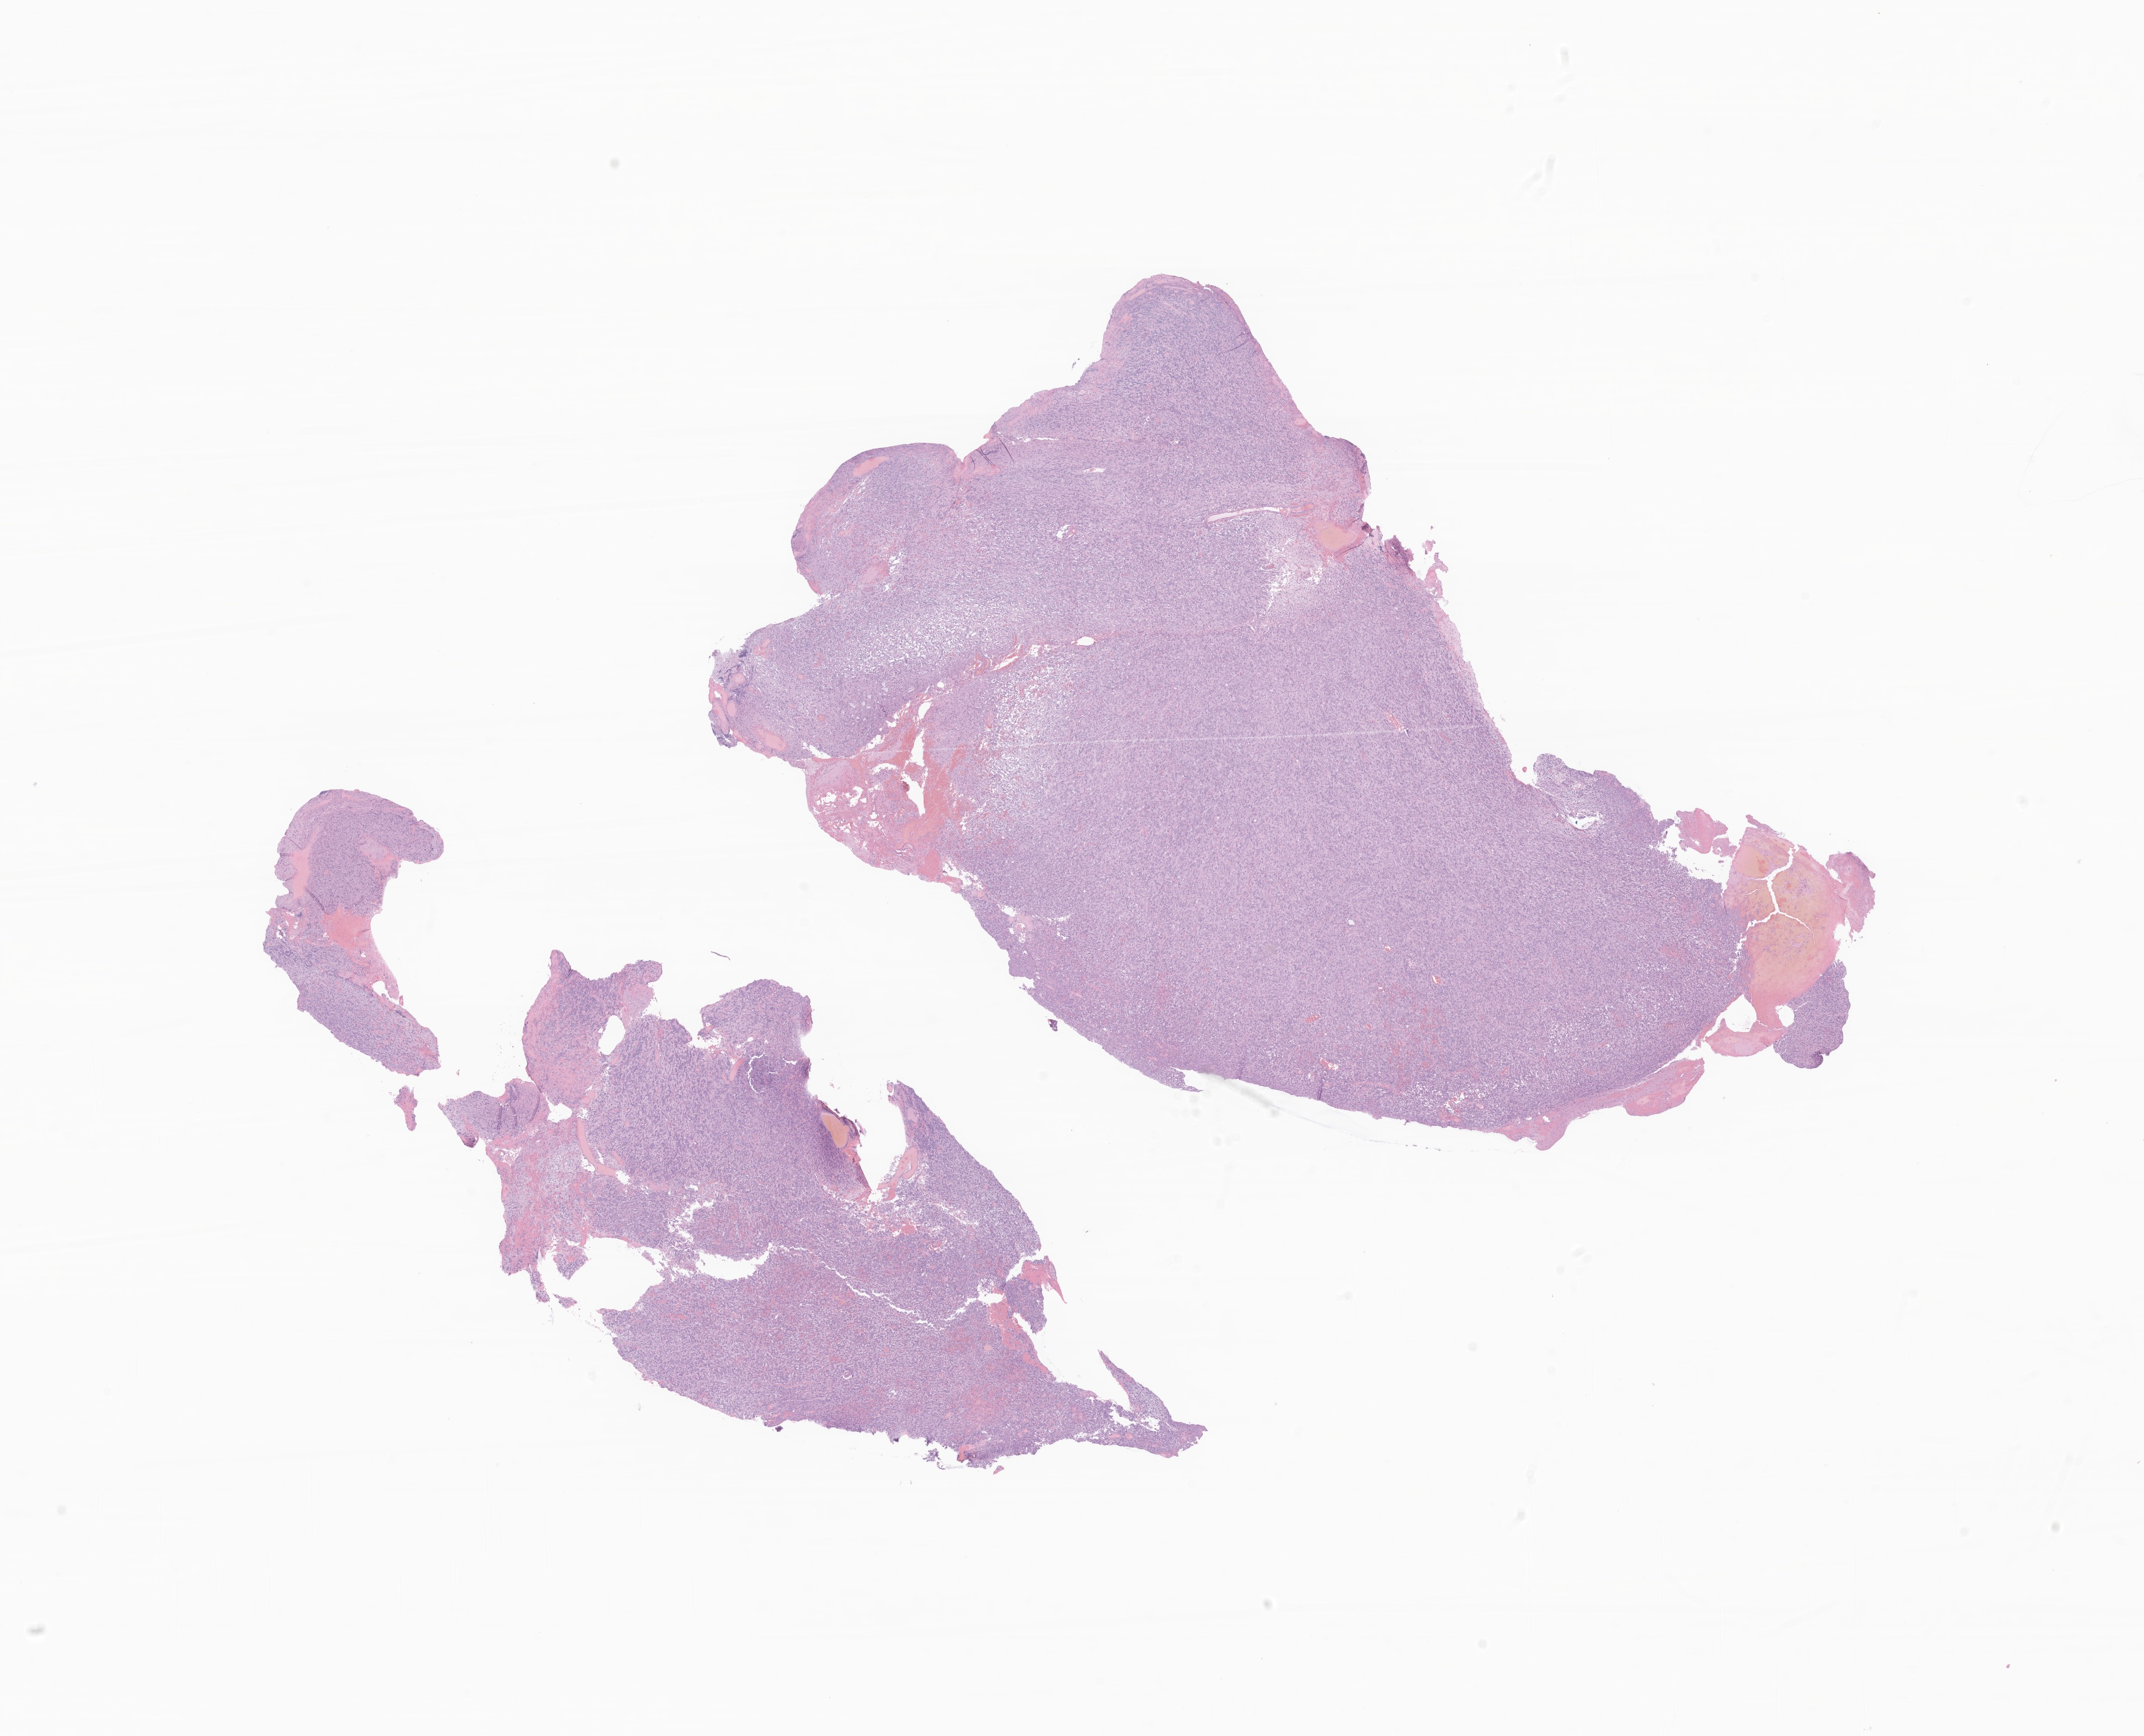
Digitized H&E-stained section of tumor tissue from the brain, a low-resolution overview of the entire scanned area, about 15.5 x 12.6 mm, FFPE section. Female patient, age 866 days (about 2.4 years).
Diagnosis: Atypical teratoid/rhabdoid tumor.